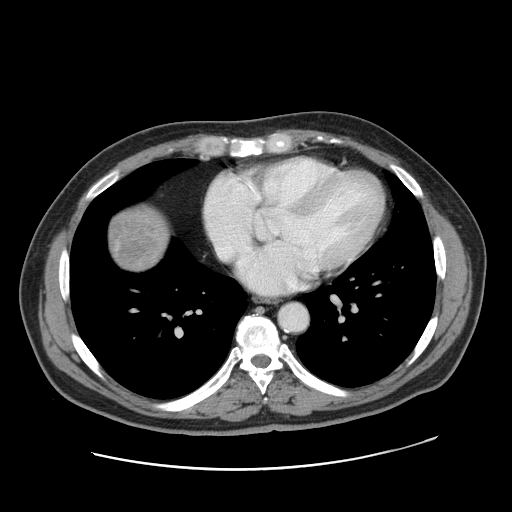
Contrast-enhanced abdominal CT, one axial slice; slice 165 of 178 in the series (ordered by position); 120 kVp; intravenous contrast given; soft-tissue window (W 400 / L 40 HU); 2.5 mm slice thickness; 512 × 512 image matrix. Male patient, age 63 years. Case-level facts recorded for this patient, not image findings: diagnosis: colorectal cancer liver metastases, imaged before liver resection; multiple liver metastases: yes; largest metastasis: 8 cm.
Annotated regions visible in this slice (outlined manually by an expert reader):
- liver: bounding box (x1, y1, x2, y2) in pixels: (108, 209, 167, 270)
- liver metastasis: (111, 208, 164, 271)